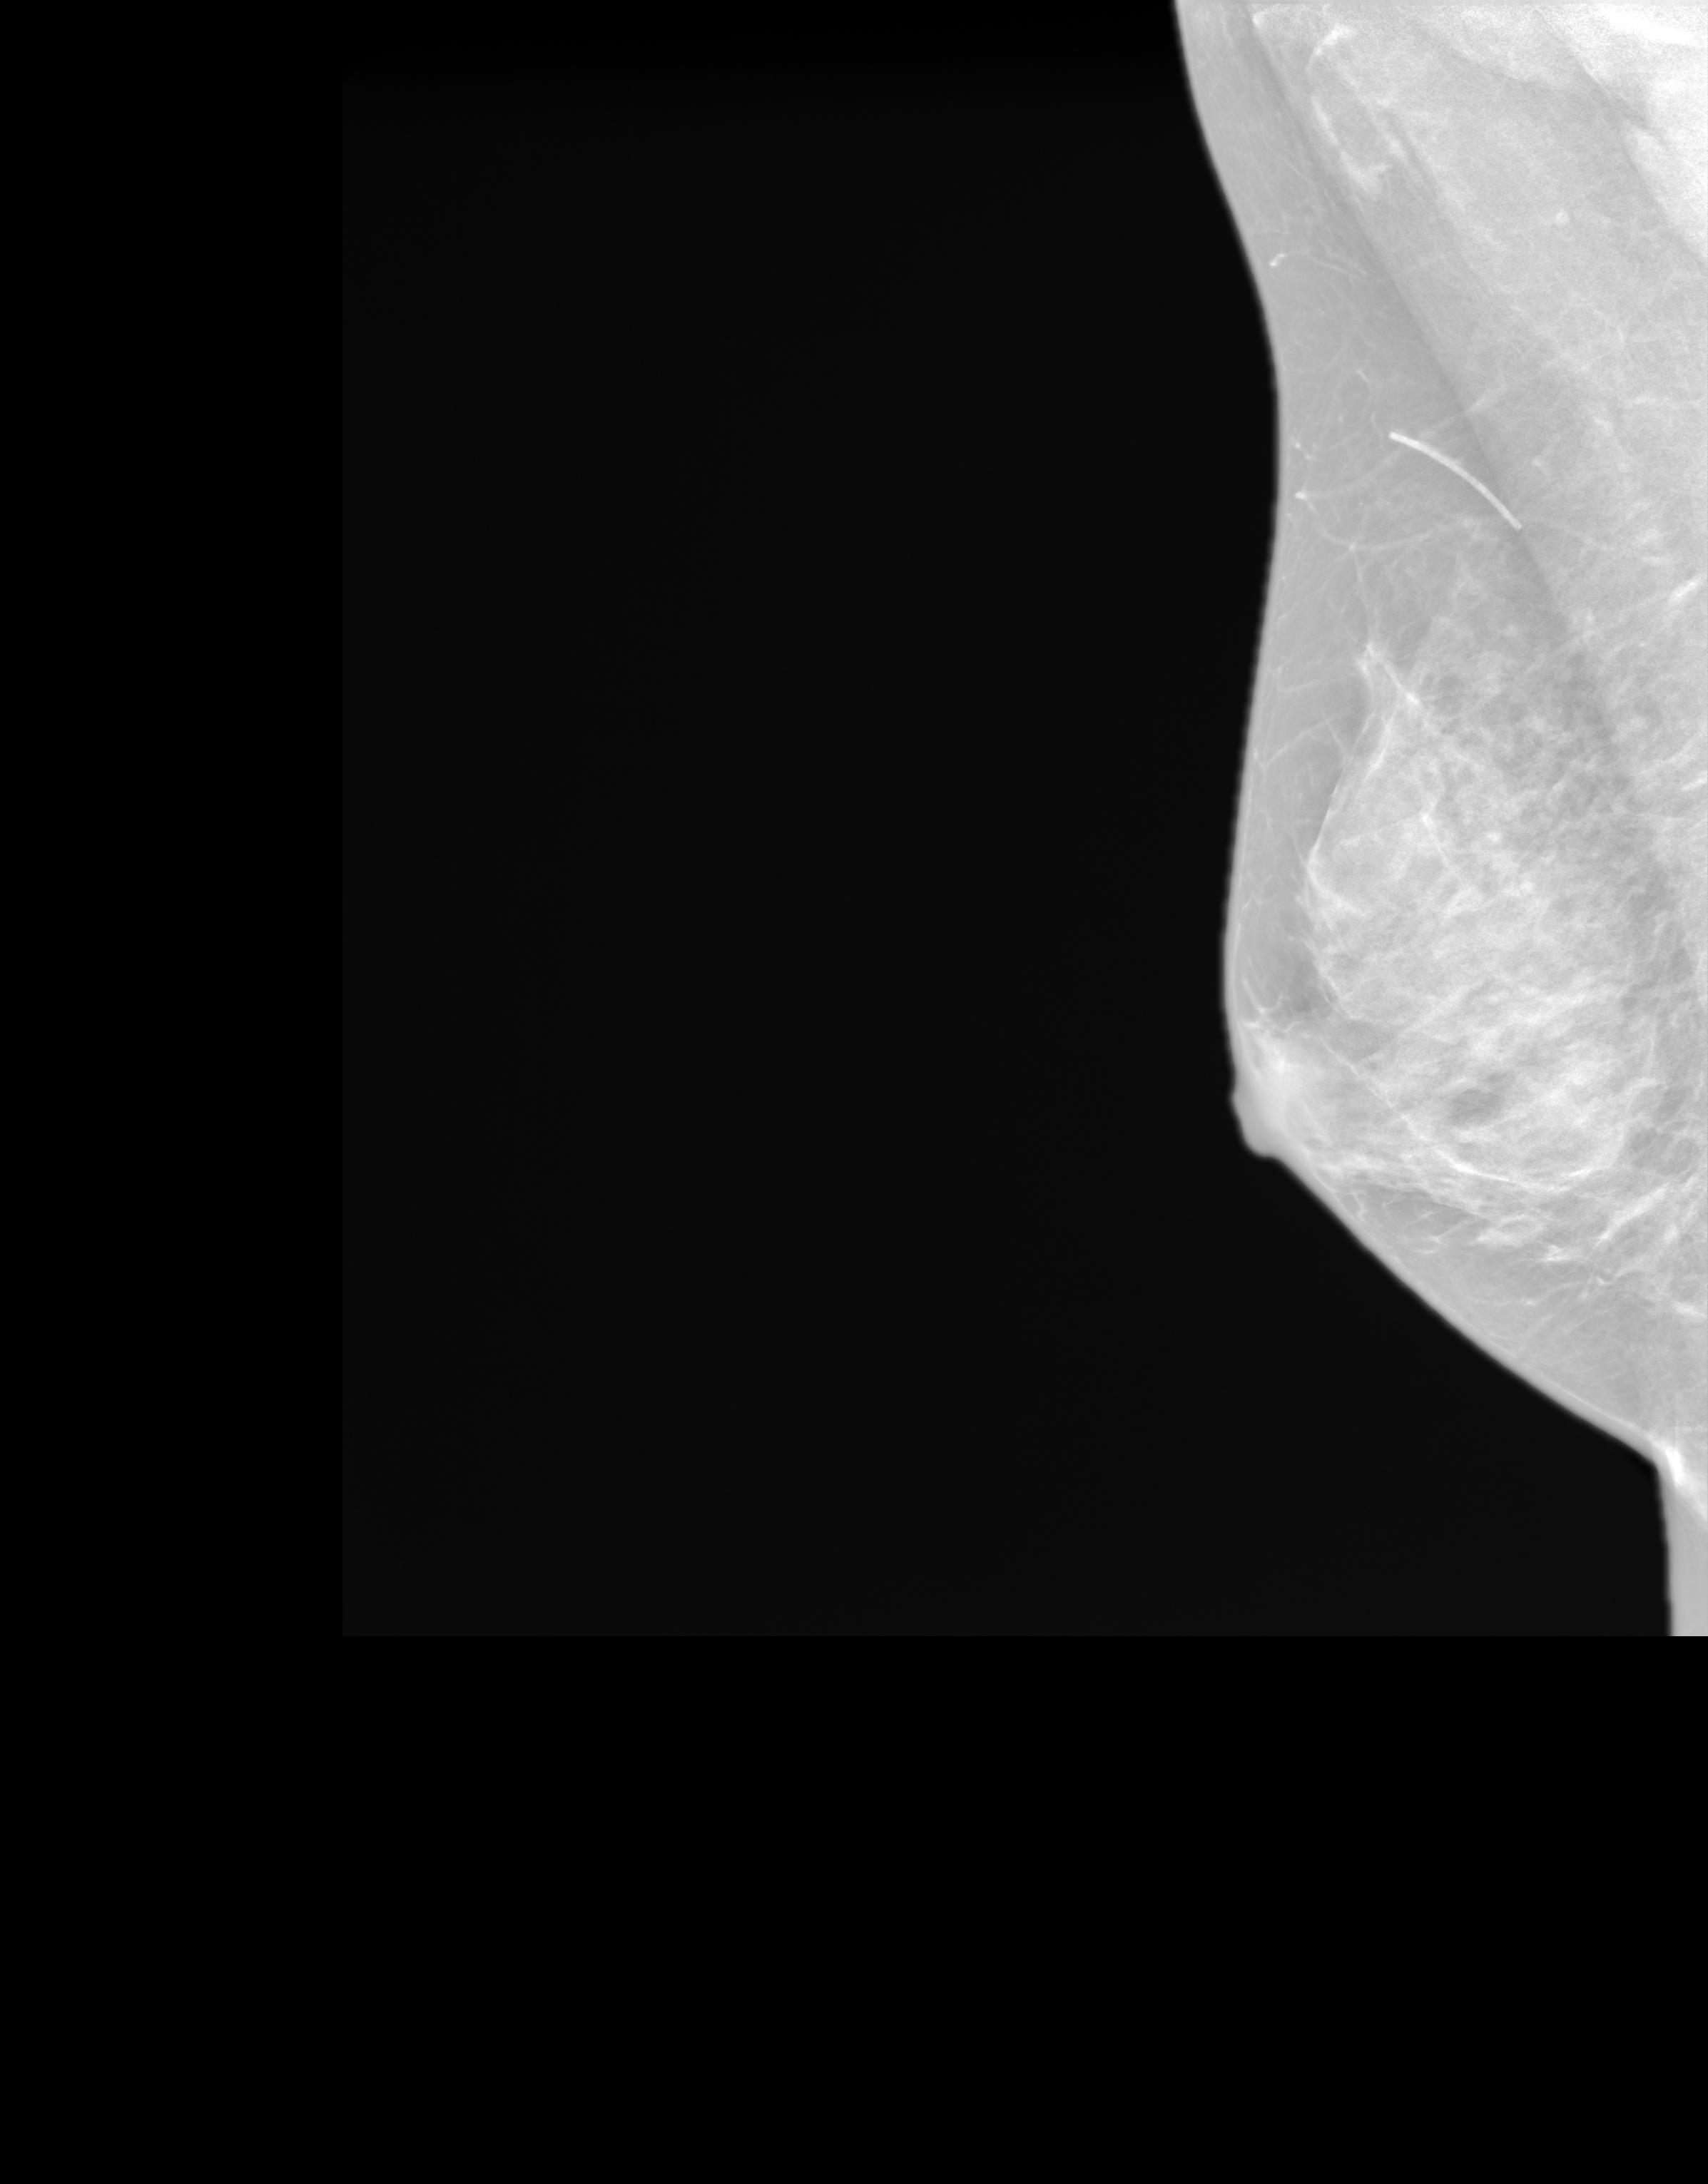
Screening examination. Patient: female, 55 years.
Image type: synthesized 2-D view from tomosynthesis. Breast: right. Projection: MLO view. BI-RADS breast density category at the screening exam (both breasts, scale 1–4): 4. Final BI-RADS assessment for this screening round (tomosynthesis exam, both breasts): category 1. Recall: no recall after this screen.